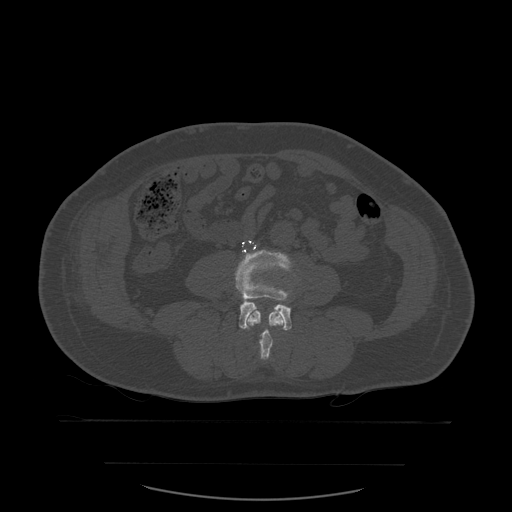
CT including the spine, one axial slice. Slice 176 of 590 in the series (ordered by position). Bone window (W 1800 / L 400 HU). 1.25 mm slice thickness. 512 × 512 image matrix, field of view 479 × 479 mm. Patient age 71 years. From the clinical record (not read from this slice): primary cancer: lung.
Outlined on this slice (semi-automatically segmented with operator editing):
- L3 vertebra: bounding box [x1, y1, x2, y2] px = [247, 311, 285, 361]
- L4 vertebra: [235, 250, 292, 331]